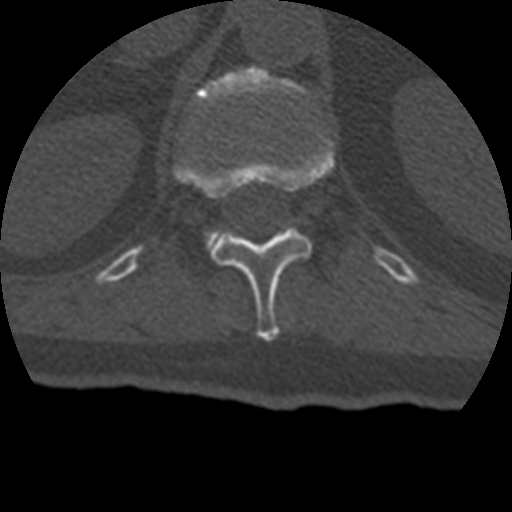
CT including the spine, one axial slice. Position 164 of 399 along the scan axis. Reconstruction kernel STANDARD. 120 kVp. Bone window (W 1800 / L 400 HU). 512 × 512 image matrix, field of view 160 × 160 mm. Patient age 69 years. From the clinical record (not read from this slice): primary cancer: prostate.
Annotated regions visible in this slice (semi-automatic segmentation, software-assisted and operator-edited):
- L1 vertebra: bounding box (x1, y1, x2, y2) in pixels: (194, 66, 307, 250)
- T12 vertebra: (175, 137, 335, 341)